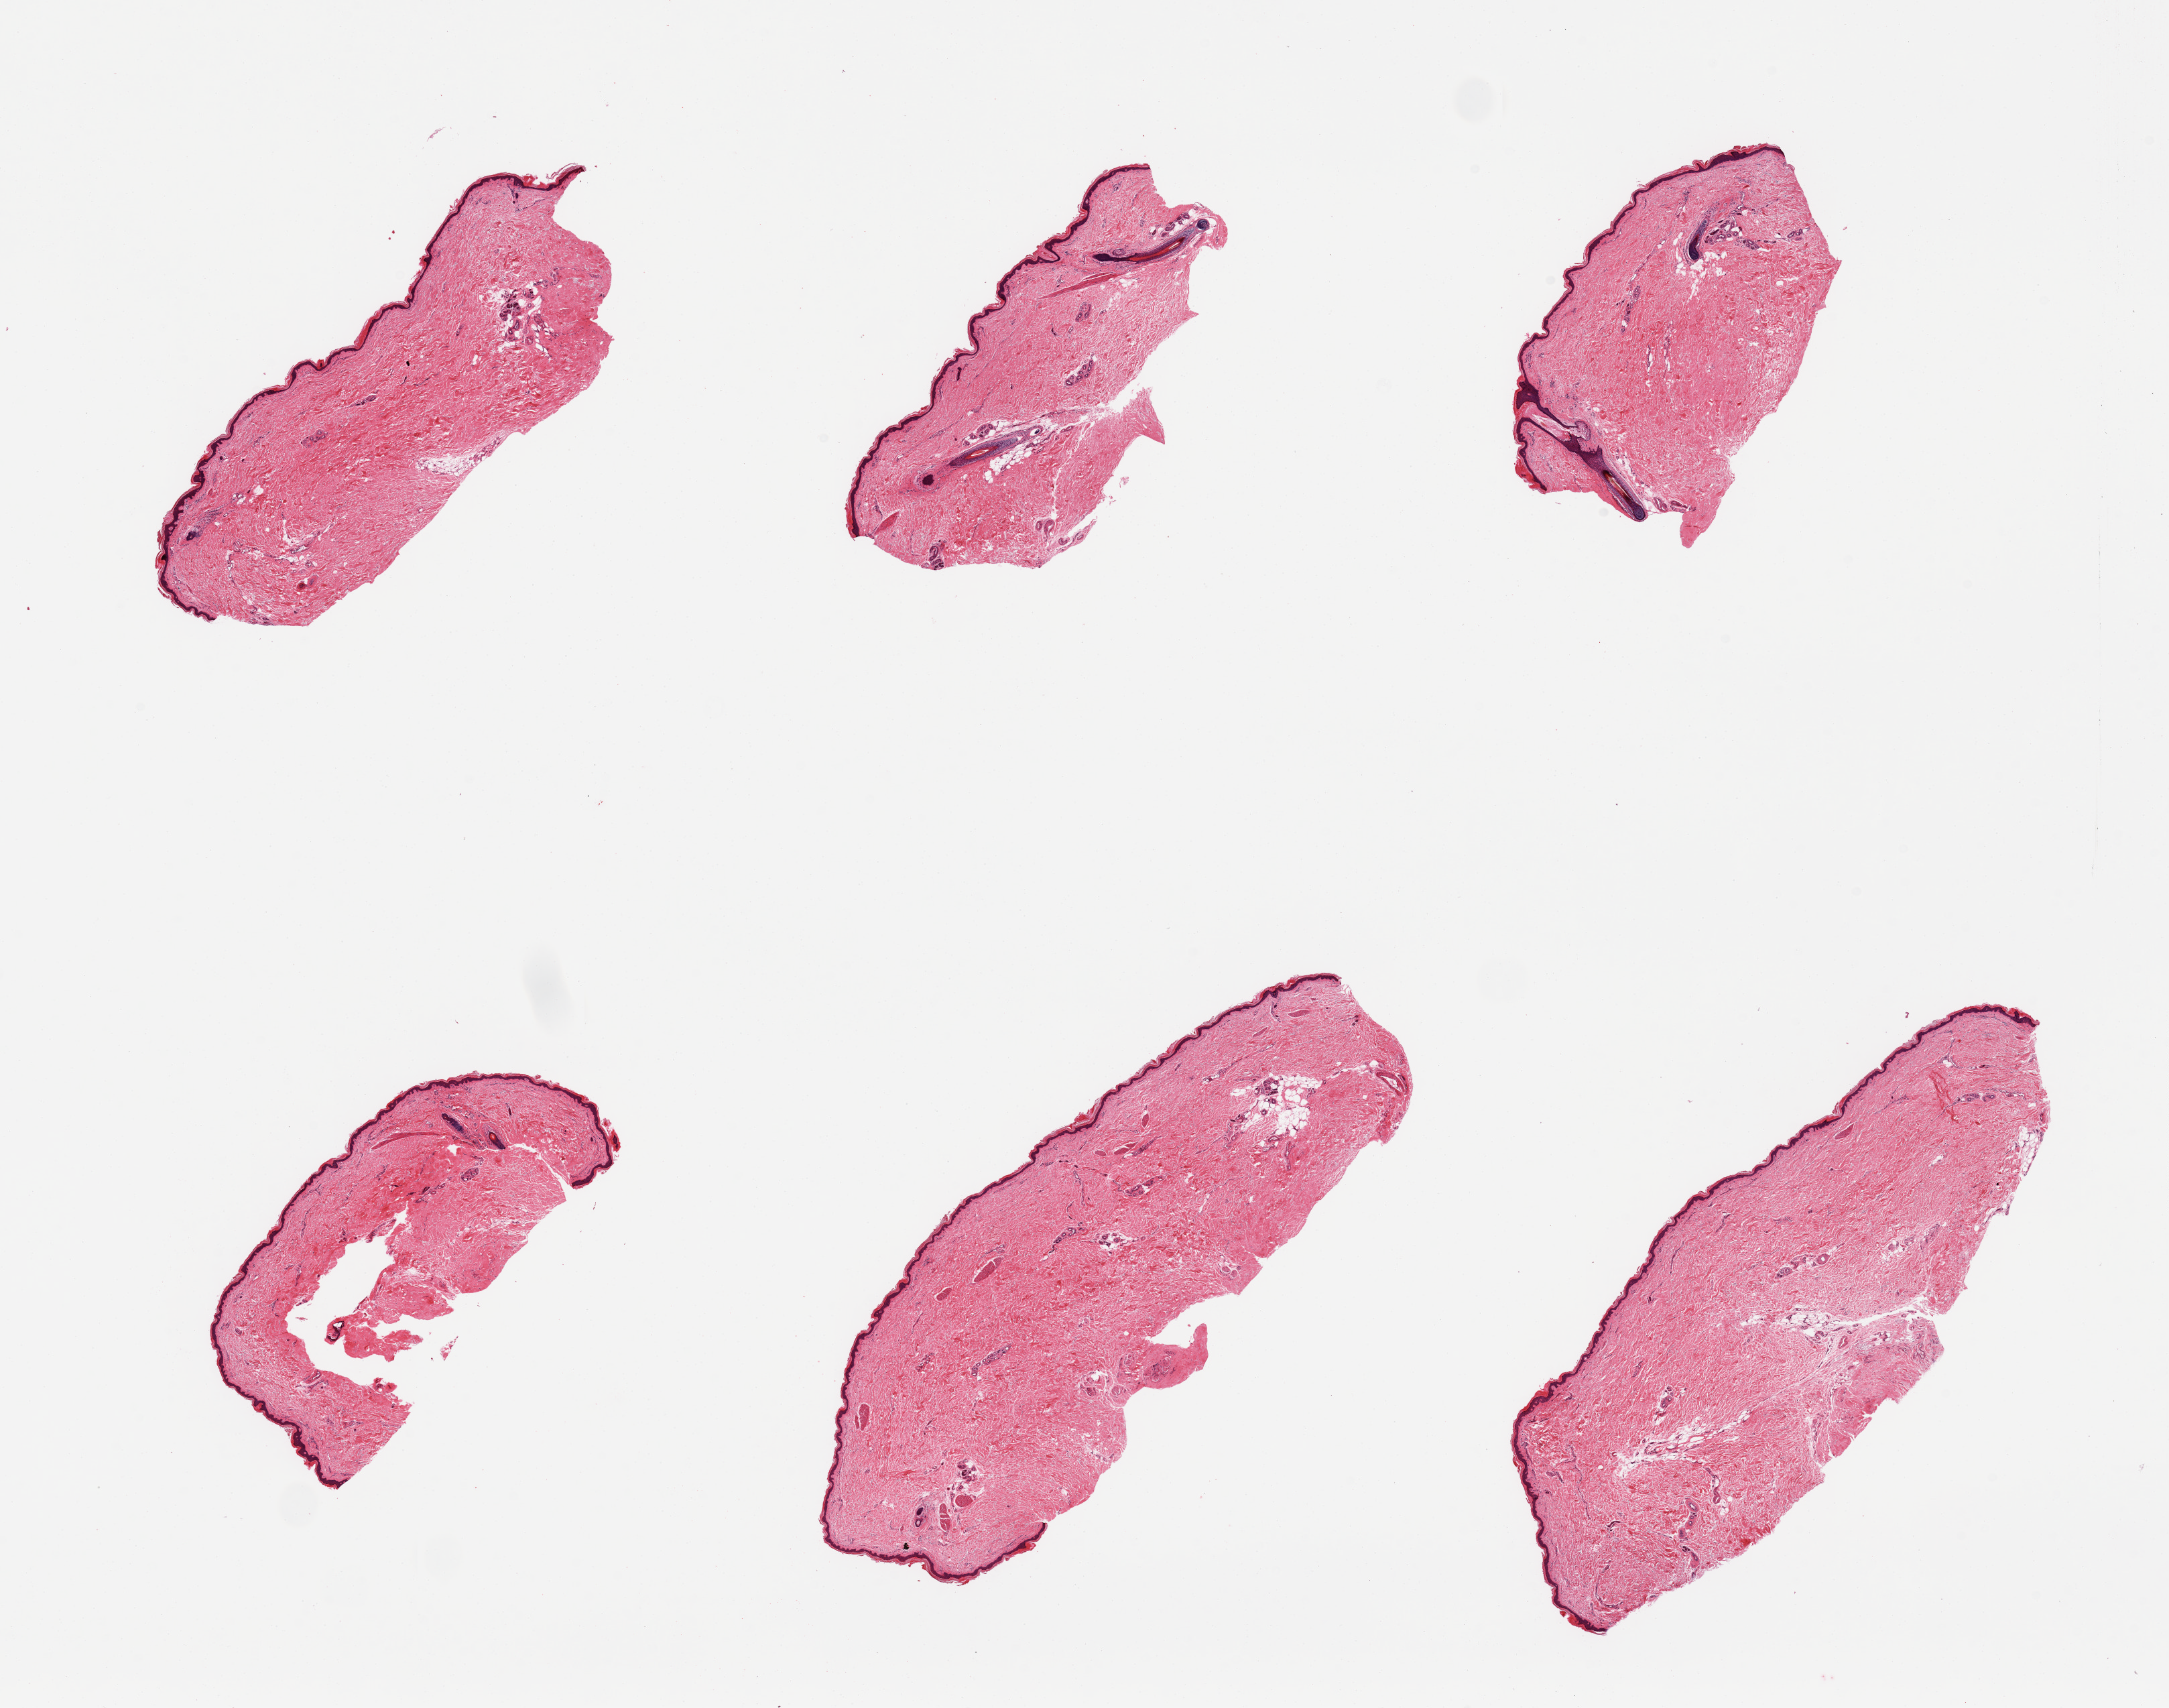
Whole-slide image, haematoxylin and eosin stain, shown as a low-resolution overview of the whole scanned area (about 25.6 x 20.2 mm, acquisition: 20x scan). PAXgene-fixed, paraffin-embedded tissue. Sampled site (target tissue): skin of lower leg. Donor tissue sample. Donor sex: male.
Reviewer comment on this tissue sample: 6 pieces, squmous epithelium is ~60-70 microns, minimal fat.